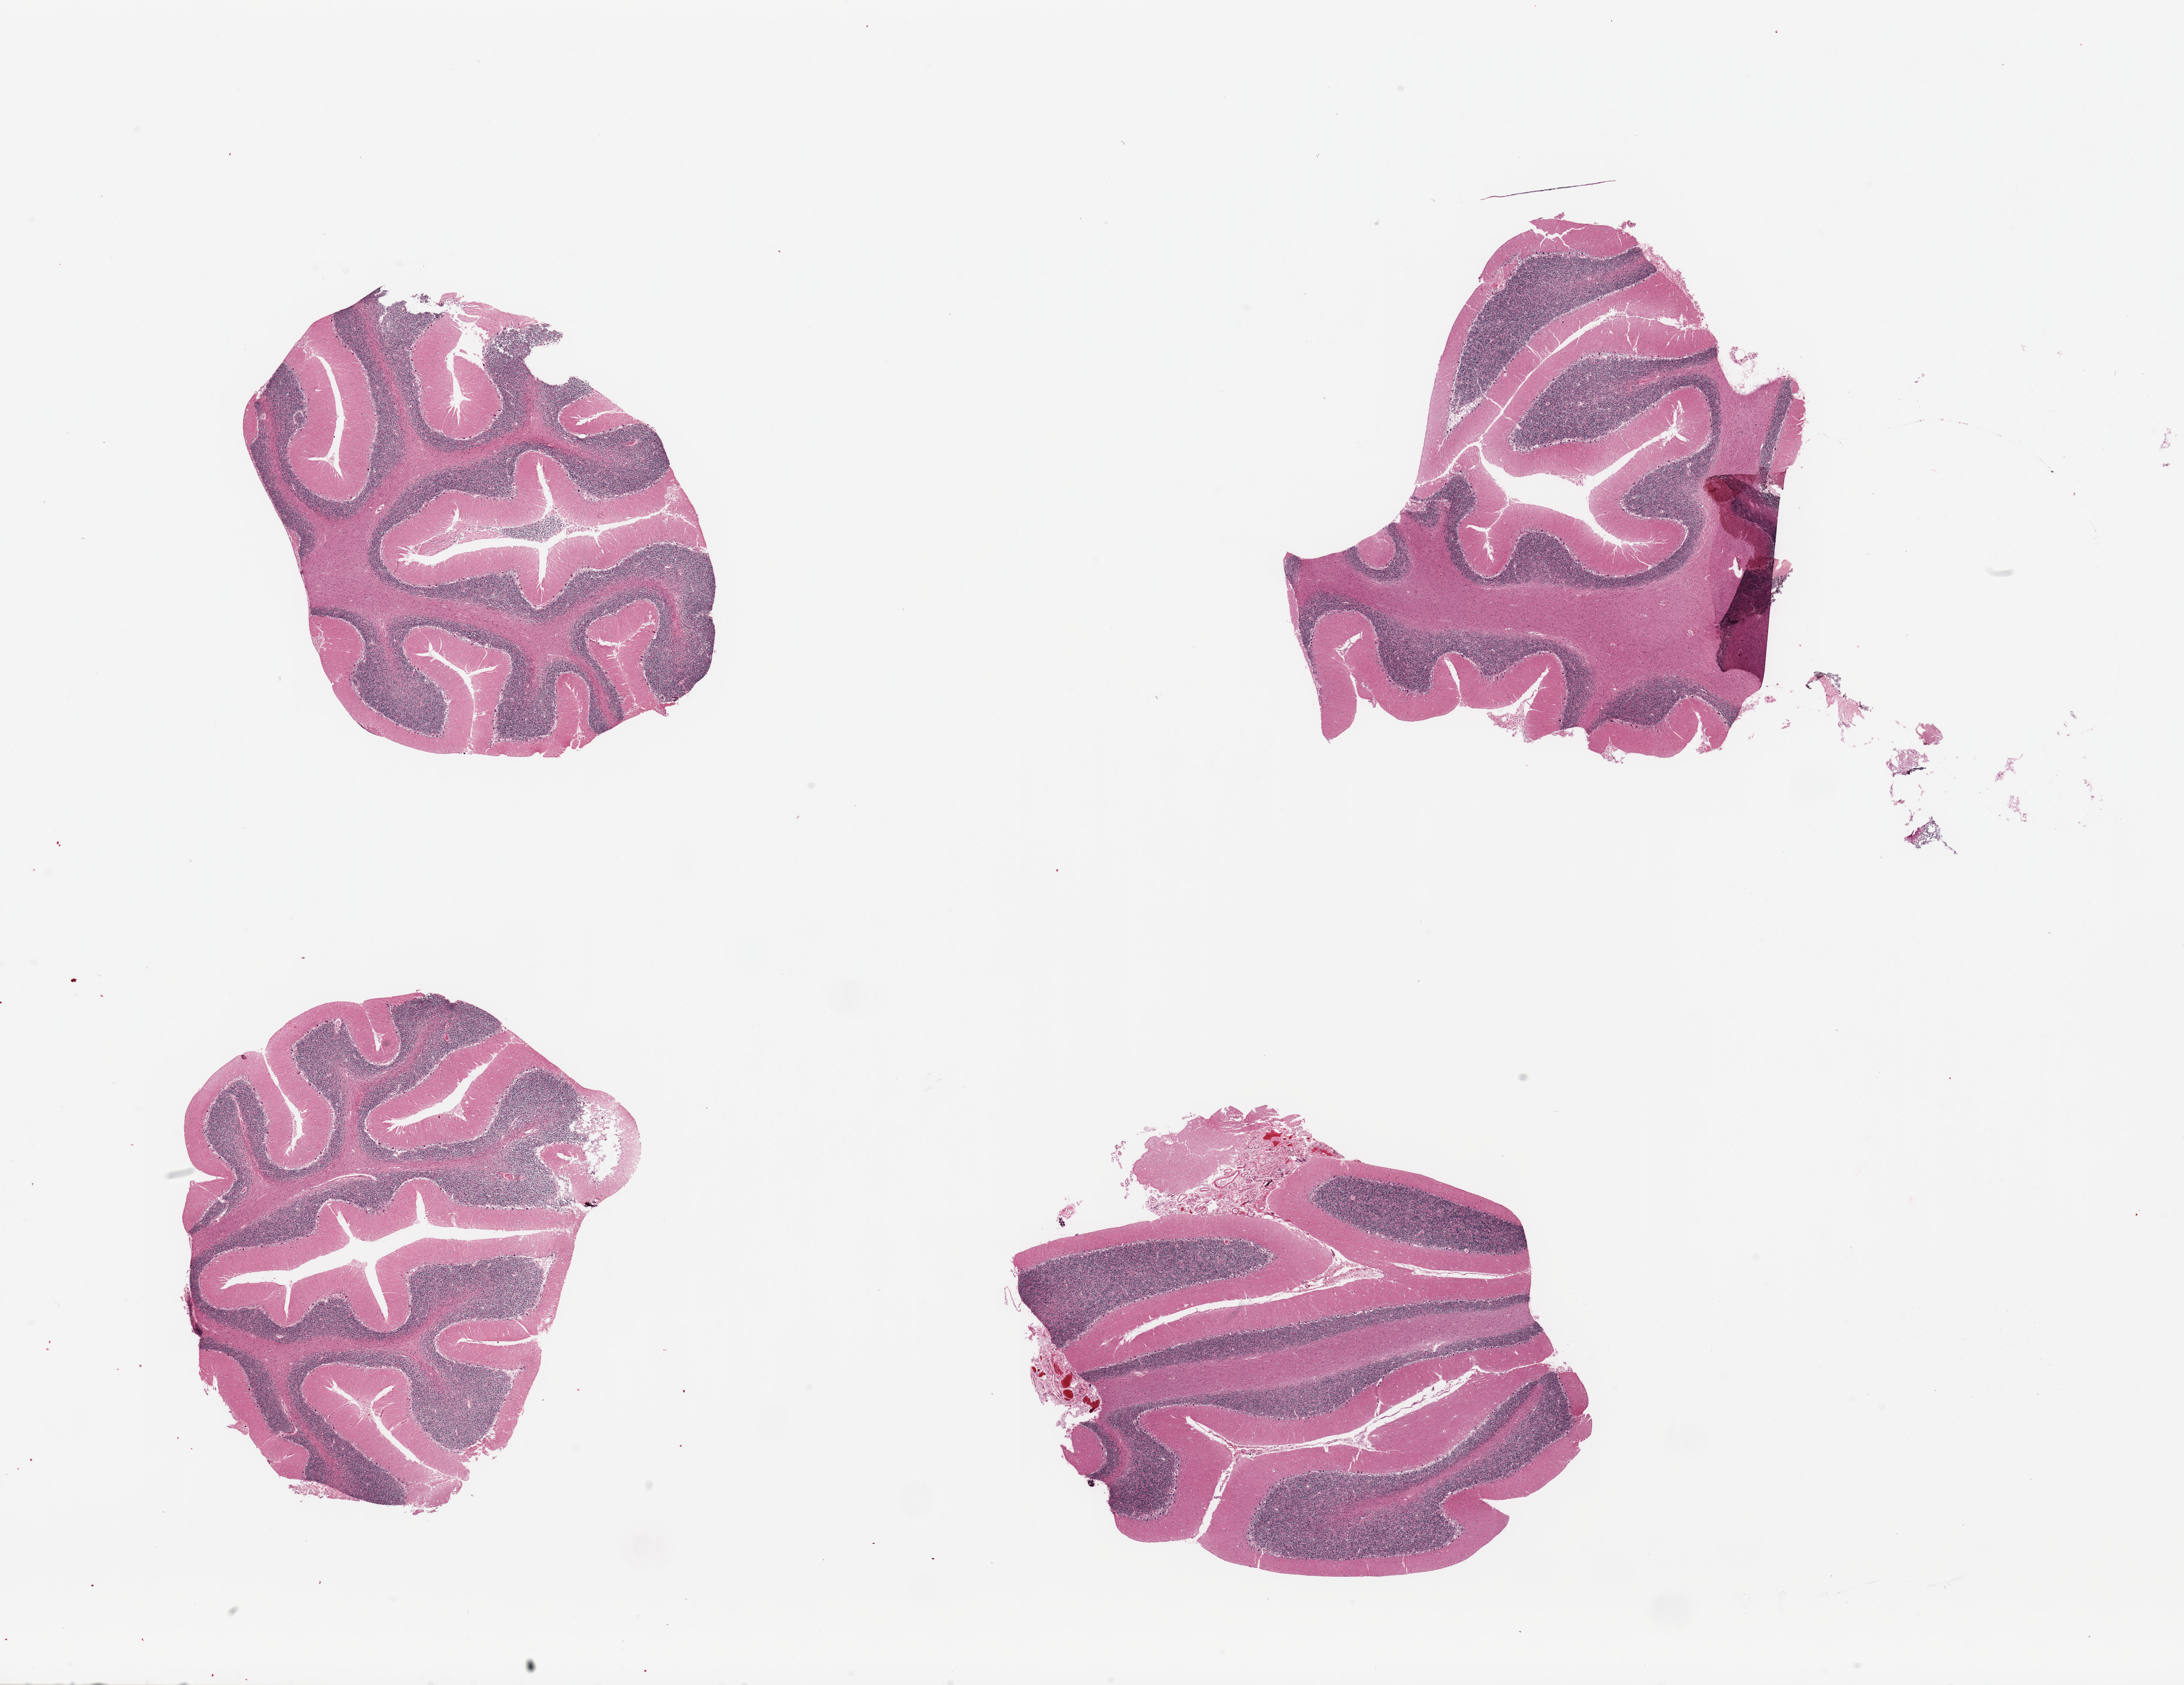
Haematoxylin and eosin whole-slide image — shown as a low-resolution overview of the whole scanned area (about 29.5 x 22.8 mm, from a 20x scan). PAXgene-fixed, paraffin-embedded tissue. Sampled site (target tissue): cerebellum. Donor tissue sample. Male donor.
Review note (as recorded): 4 pieces; Purkinje cells present; one piece with attached congested meninges.